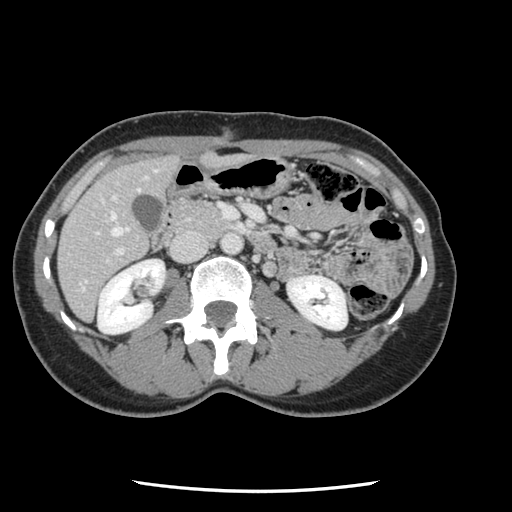
Contrast-enhanced abdominal CT, one axial slice. Slice 41 of 134 in the series (ordered by position). 120 kVp. Intravenous contrast given. Soft-tissue window (W 400 / L 40 HU). 2.5 mm slice thickness. 512 × 512 image matrix. Female patient, age 43 years. From the clinical record (not read from this slice): diagnosis: colorectal cancer liver metastases, imaged before liver resection; multiple liver metastases: yes; largest metastasis: 3.4 cm; disease in both lobes: yes.
Structures marked on this image (expert manual segmentation):
- hepatic veins: bounding box <110,189,140,237> (left, top, right, bottom; pixels)
- liver: <59,156,179,319>
- planned liver remnant (the part of the liver to remain after resection): <59,157,179,320>
- portal vein (with intrahepatic branches): <94,202,263,263>